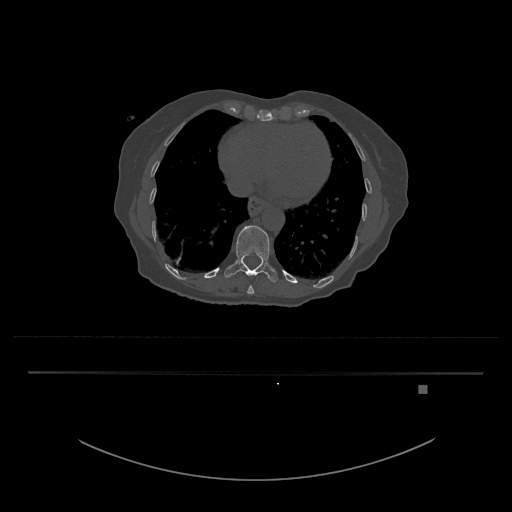
CT including the spine, one axial slice; slice 674 of 797 in the series (ordered by position); reconstruction kernel Br40s/3; 120 kVp; bone window (W 1800 / L 400 HU); 0.5 mm slice thickness; 512 × 512 image matrix, field of view 500 × 500 mm. Patient: female, 57 years. Case-level facts recorded for this patient, not image findings: primary cancer: cervical.
Outlined on this slice (semi-automatically segmented with operator editing):
- T10 vertebra: bounding box (x1, y1, x2, y2) in pixels: (247, 275, 255, 294)
- T11 vertebra: (224, 225, 278, 282)